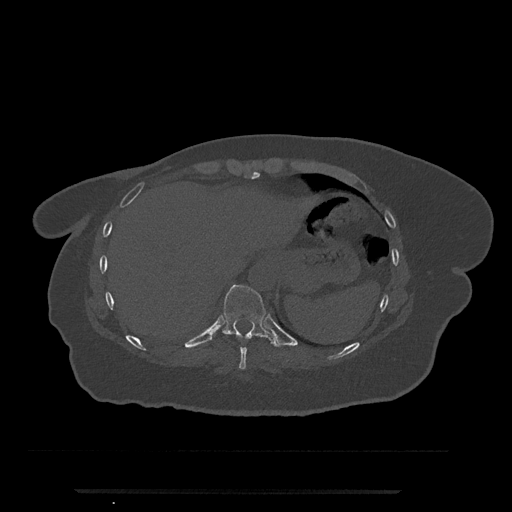
CT including the spine, one axial slice; reconstruction kernel Br40s/3; bone window (W 1800 / L 400 HU); 0.5 mm slice thickness; 512 × 512 image matrix, field of view 440 × 440 mm. Patient: female, 51 years. Case-level facts recorded for this patient, not image findings: primary cancer: neuro; vertebrae with lytic lesions (as recorded): T8.
Structures marked on this image (semi-automatic segmentation, software-assisted and operator-edited):
- T10 vertebra: bounding box (x1, y1, x2, y2) in pixels: (222, 284, 277, 347)
- T9 vertebra: (239, 347, 247, 370)